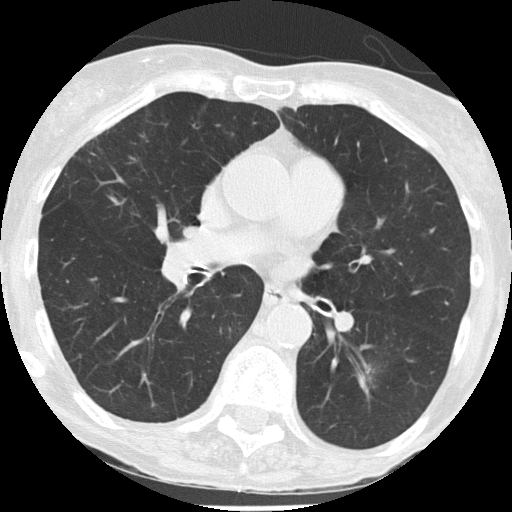
Chest CT (low-dose screening protocol), one axial image. Third screening round (two years after baseline). Lung window (W 1500 / L -600 HU). Lung (sharp) reconstruction kernel (FC51). 512 × 512 image matrix. Female participant, aged 68 years at enrolment. Former smoker at enrolment.
- Expert-annotated lung lesion, bounding box [x1, y1, x2, y2] px = [333, 345, 400, 406].
- Screening reader's record for this exam (one nodule recorded; not confirmed to be the boxed lesion): non-calcified nodule or mass ≥4 mm, left lower lobe, 11 × 9 mm, spiculated (stellate) margins, soft tissue attenuation, pre-existing on the prior screen: yes; interval growth: yes.
- Lung cancer was diagnosed 164 days after this screen: non-small cell carcinoma, left lower lobe, poorly differentiated (G3), stage IA (AJCC 6th edition), 10 mm at pathology.